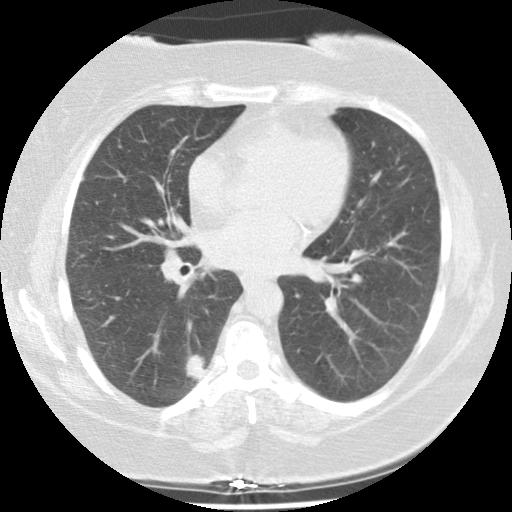
Low-dose screening chest CT, one axial slice; position 75 of 131 along the scan axis; reconstruction kernel STANDARD; lung window (W 1500 / L -600 HU); 512 × 512 image matrix, field of view 320 × 320 mm.
Structures marked on this image (expert manual segmentation):
- lesion 1 (tumor, lower lobe of right lung): bounding box (x1, y1, x2, y2) in pixels: (184, 351, 205, 381)